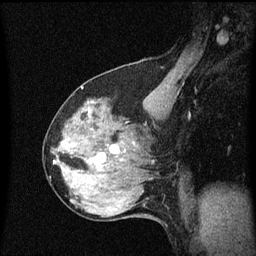
Breast MRI (dynamic contrast-enhanced), one sagittal slice. Position 35 of 60 along the scan axis. Dynamic contrast-enhanced series, image 2 of 3 at this slice position (ordered by acquisition). 1.5 T. TE 4.2 ms, TR 8.4 ms. 256 × 256 image matrix. Patient: female, 64 years. Case-level facts recorded for this patient, not image findings: setting: breast cancer imaged before/during neoadjuvant chemotherapy; receptor status: HR-positive, HER2-negative.
Annotated regions visible in this slice (semi-automatic segmentation, software-assisted and operator-edited):
- analysis volume of interest (the breast-tissue region the enhancement analysis was run in; not a lesion): box from (x=56, y=92) to (x=141, y=175) px
- tumour enhancement mask (voxels above the 70 % enhancement threshold inside the analysis volume of interest): (x=96, y=158)–(x=101, y=167)